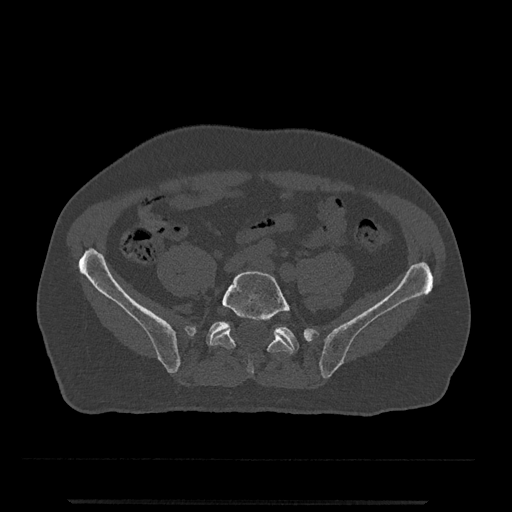
CT including the spine, one axial slice; position 57 of 797 along the scan axis; reconstruction kernel Br40s/3; 120 kVp; bone window (W 1800 / L 400 HU); 0.5 mm slice thickness; 512 × 512 image matrix. Patient: male, 63 years. From the clinical record (not read from this slice): primary cancer: prostate.
Structures marked on this image (semi-automatically segmented with operator editing):
- L5 vertebra: bounding box <210,271,293,375> (left, top, right, bottom; pixels)